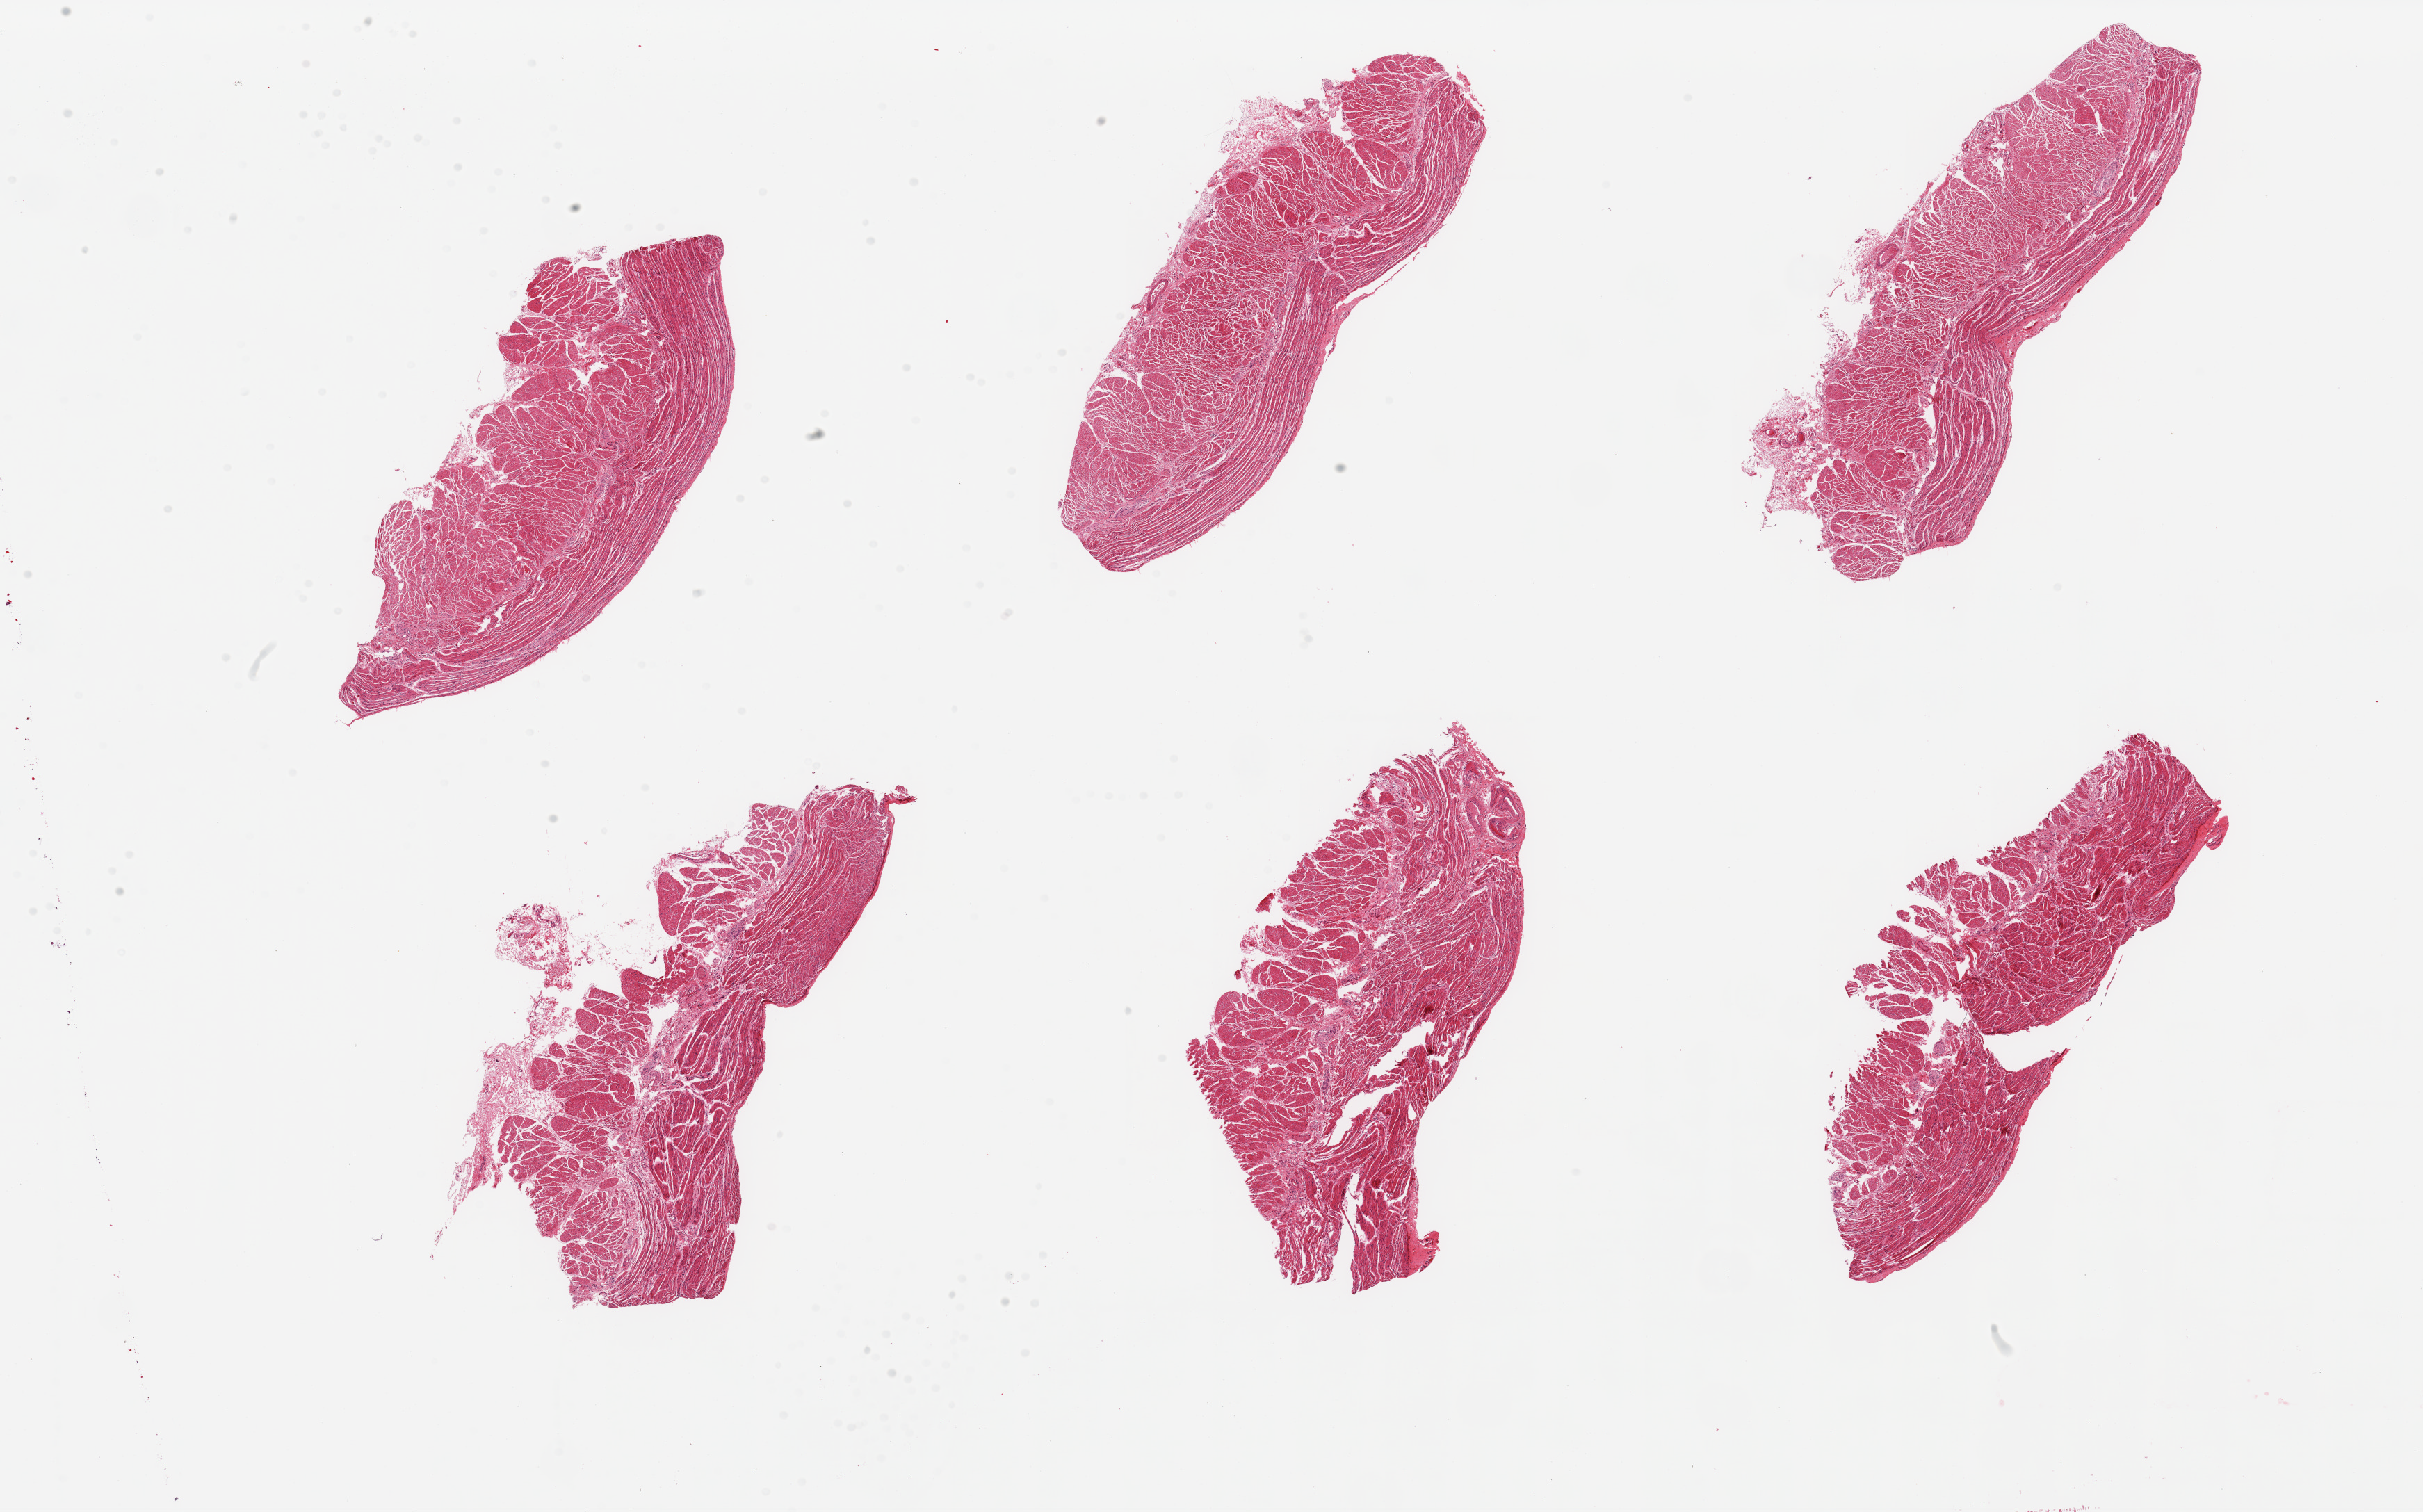
Hematoxylin and eosin (H&E) whole-slide image — low-resolution overview of the scanned area, about 27.6 x 17.2 mm; PAXgene-fixed paraffin-embedded (PFPE) section; section of gastroesophageal junction (target tissue); tissue donor sample. Female donor.
Reviewer comment on this tissue sample: 6 pieces; well dissected muscle.